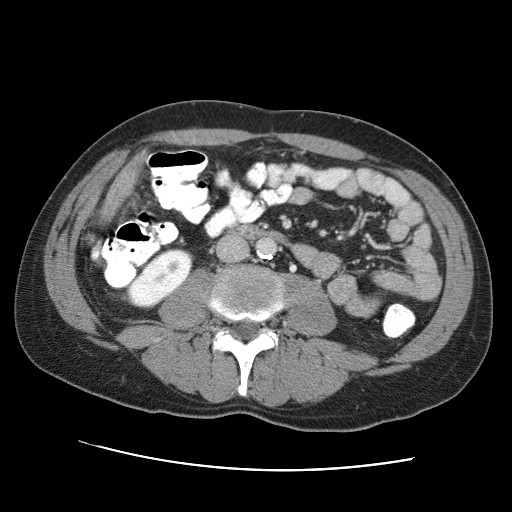
Contrast-enhanced abdominal CT (liver protocol), one axial slice; slice 5 of 95 in the series (ordered by position); one of 2 acquisitions stored at this slice position; soft-tissue window (W 400 / L 40 HU); 2.5 mm slice thickness; 512 × 512 image matrix, field of view 360 × 360 mm. Case-level facts recorded for this patient, not image findings: diagnosis: hepatocellular carcinoma (patient treated with transarterial chemoembolisation; whether this scan precedes or follows treatment is not stated here); TNM stage (as recorded): Stage-IVA; Child-Pugh class: A; tumour differentiation: moderately differentiated; tumour nodularity: multinodular.
Annotated regions visible in this slice (semi-automatic segmentation, software-assisted and operator-edited):
- liver parenchyma outside the tumour (the mass and vessels are separate outlines, so this box may not span the whole liver): bounding box [x1, y1, x2, y2] px = [102, 156, 140, 219]